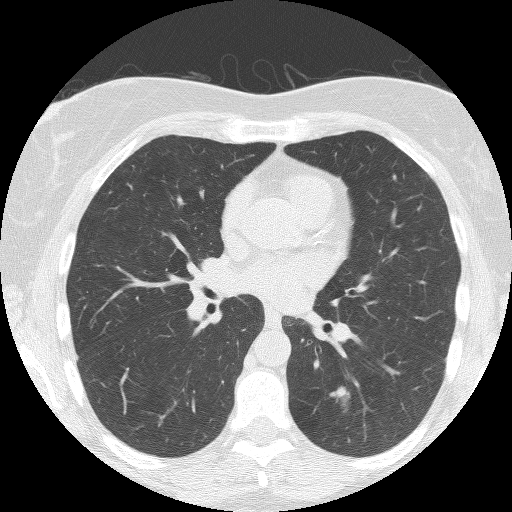
Axial slice from a low-dose chest CT screening exam, second annual screen, lung window (W 1500 / L -600 HU), 2.5 mm slice thickness, slice 70 of 150 in the series. Female, age 60 years at enrolment. Former smoker at enrolment.
Lesion marked by an expert reader, bounding box [x1, y1, x2, y2] px = [316, 381, 361, 424]. The exam's reader record, not a measurement of the box and not confirmed to be the same lesion: non-calcified nodule or mass ≥4 mm, left lower lobe, 16 × 7 mm, smooth margins, soft tissue attenuation, pre-existing on the prior screen: no. Participant outcome: lung cancer diagnosed 54 days after this screen — small cell carcinoma, NOS, left lower lobe, stage IIA (AJCC 6th edition), 12 mm at pathology.